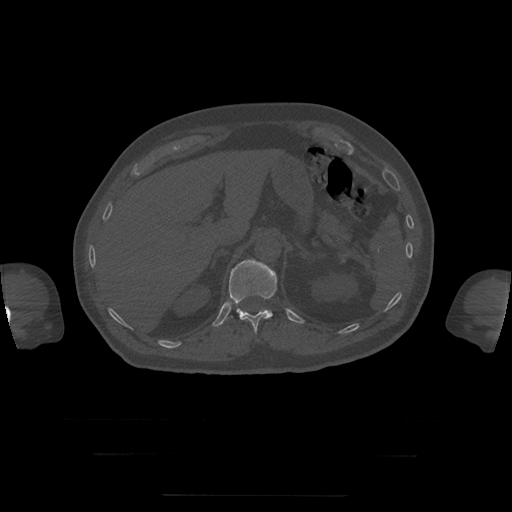
CT including the spine, one axial slice; position 72 of 397 along the scan axis; reconstruction kernel STANDARD; bone window (W 1800 / L 400 HU); 1.25 mm slice thickness; 512 × 512 image matrix, field of view 510 × 510 mm. Patient age 73 years. Case-level facts recorded for this patient, not image findings: primary cancer: prostate.
Structures marked on this image (semi-automatic segmentation, software-assisted and operator-edited):
- T12 vertebra: box from (x=229, y=260) to (x=277, y=334) px